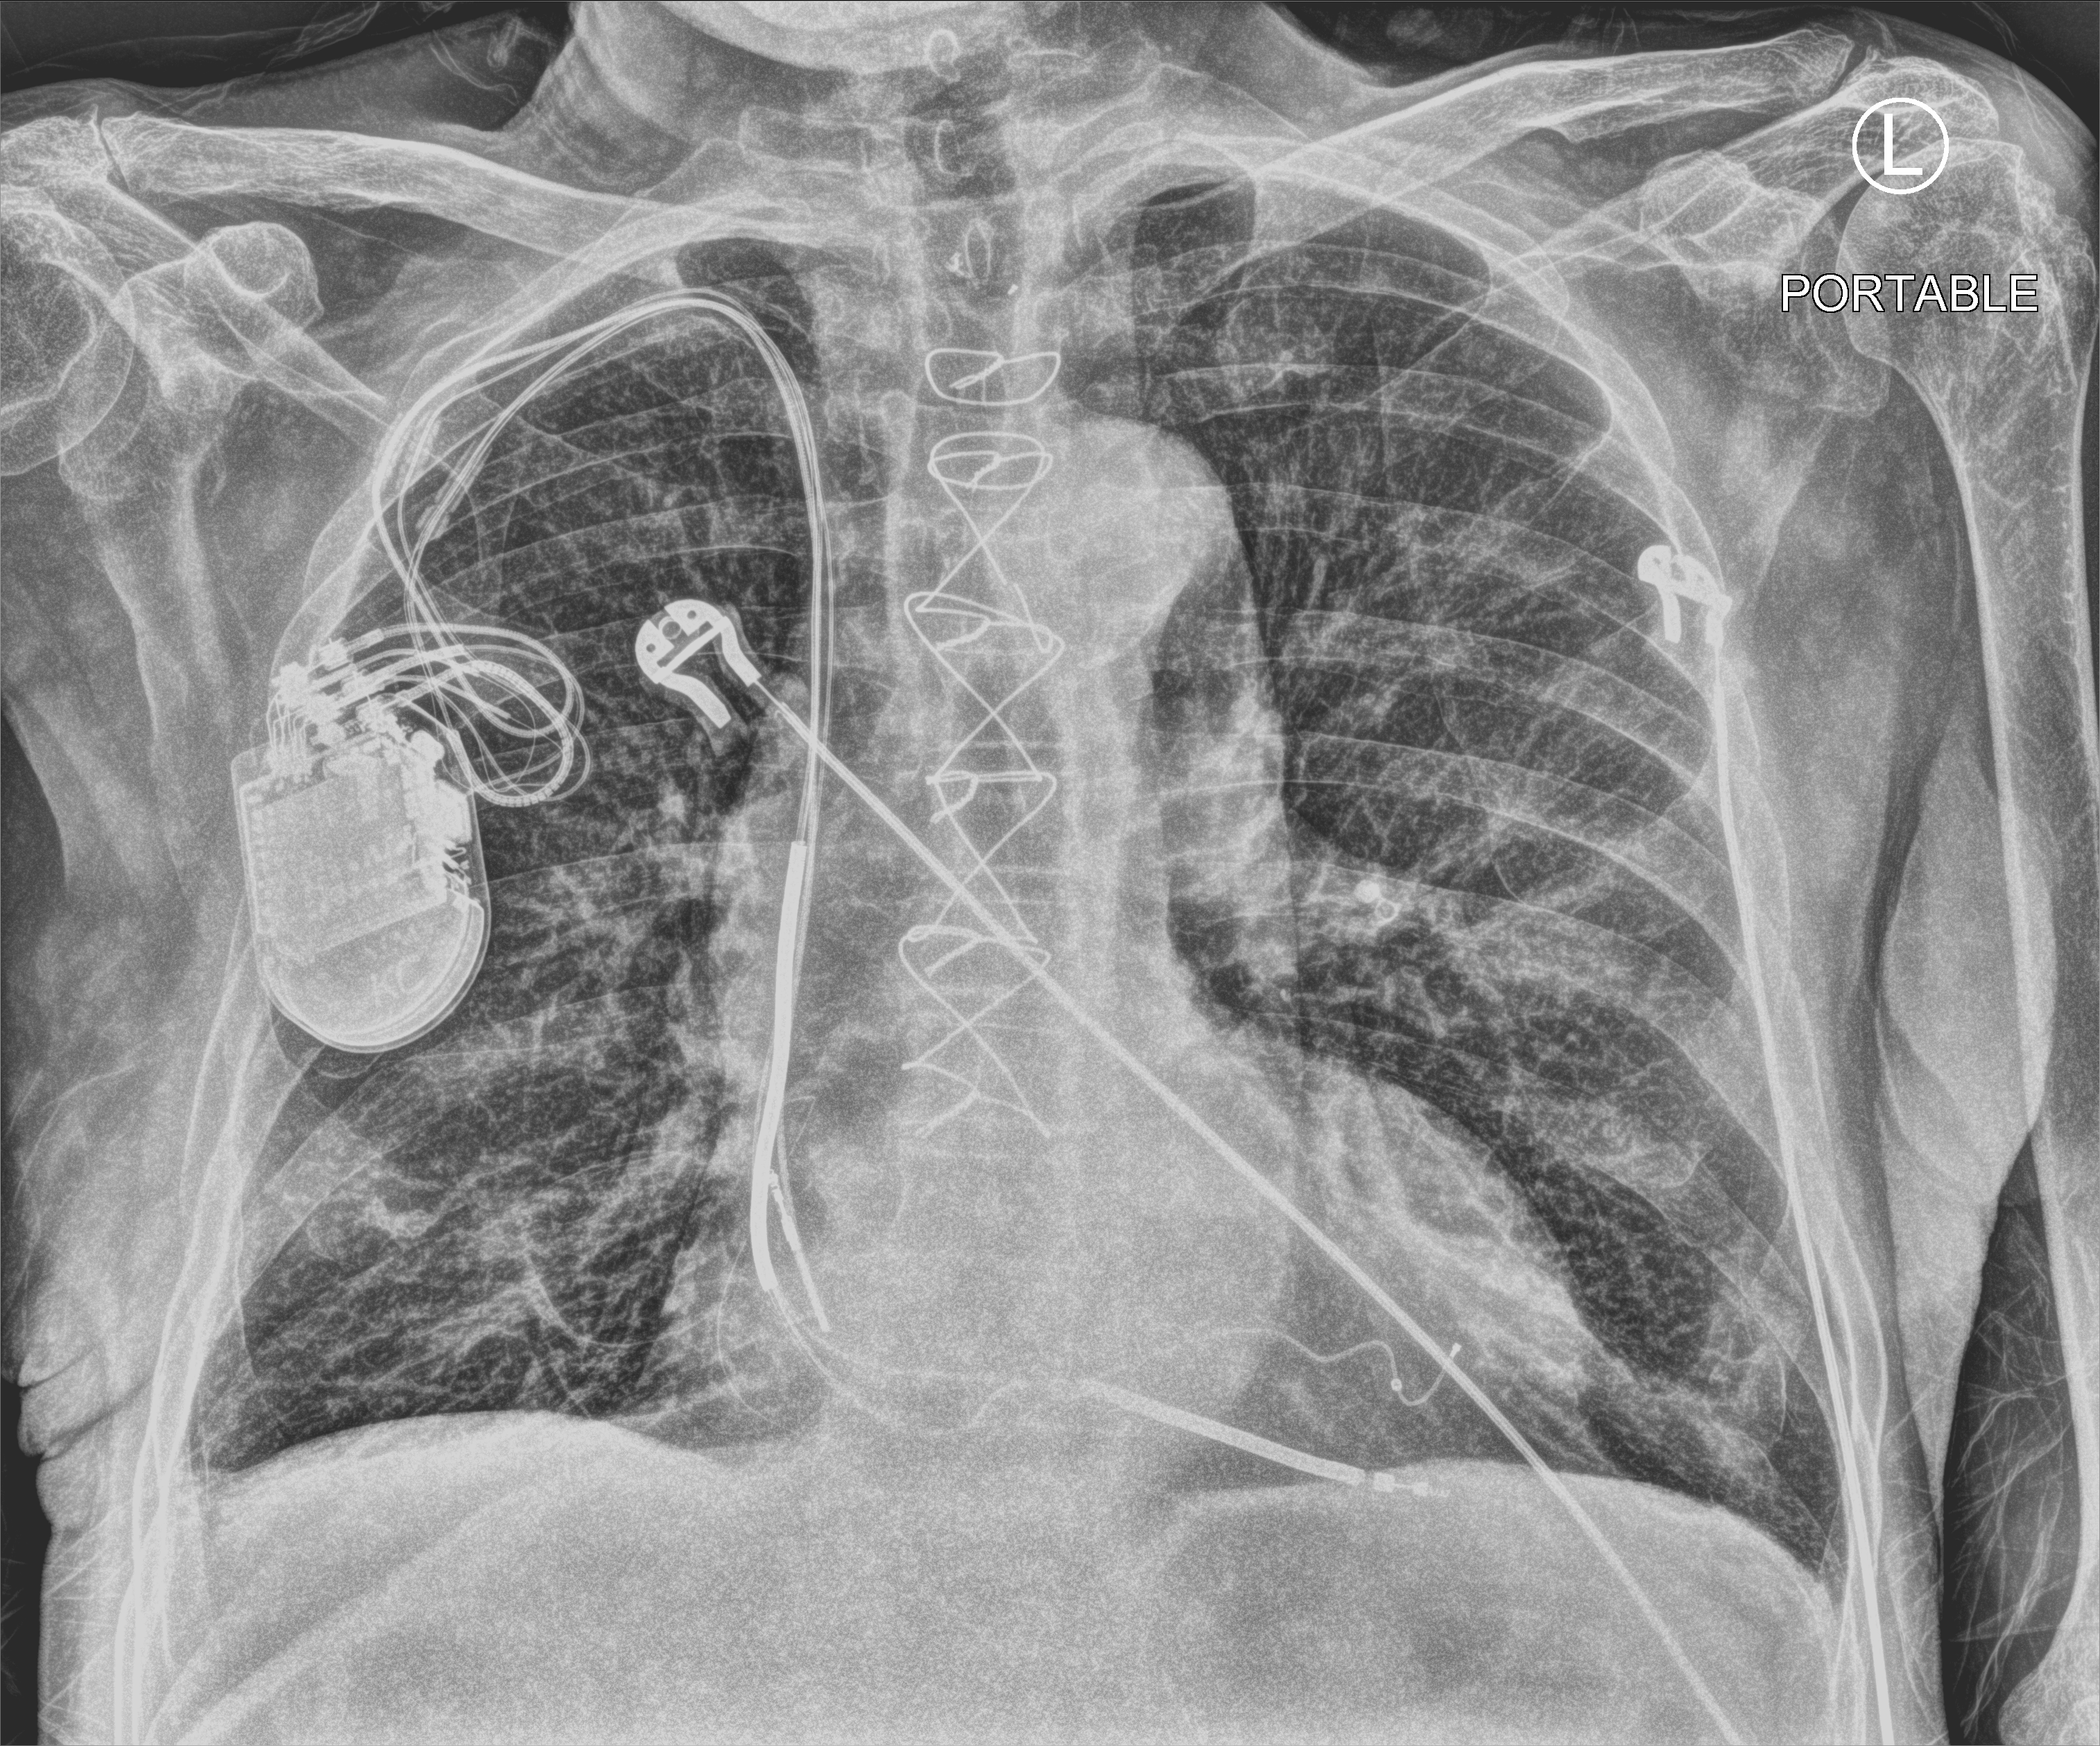
Portable chest radiograph; anteroposterior (AP) projection. Male patient hospitalised with COVID-19, age 75–90 years.
Hospital-stay facts (about this admission, not read from this image; timing relative to this image not recorded): admitted to intensive care during this hospital stay: no; length of hospital stay: 3 days; mechanically ventilated during this hospital stay: no.